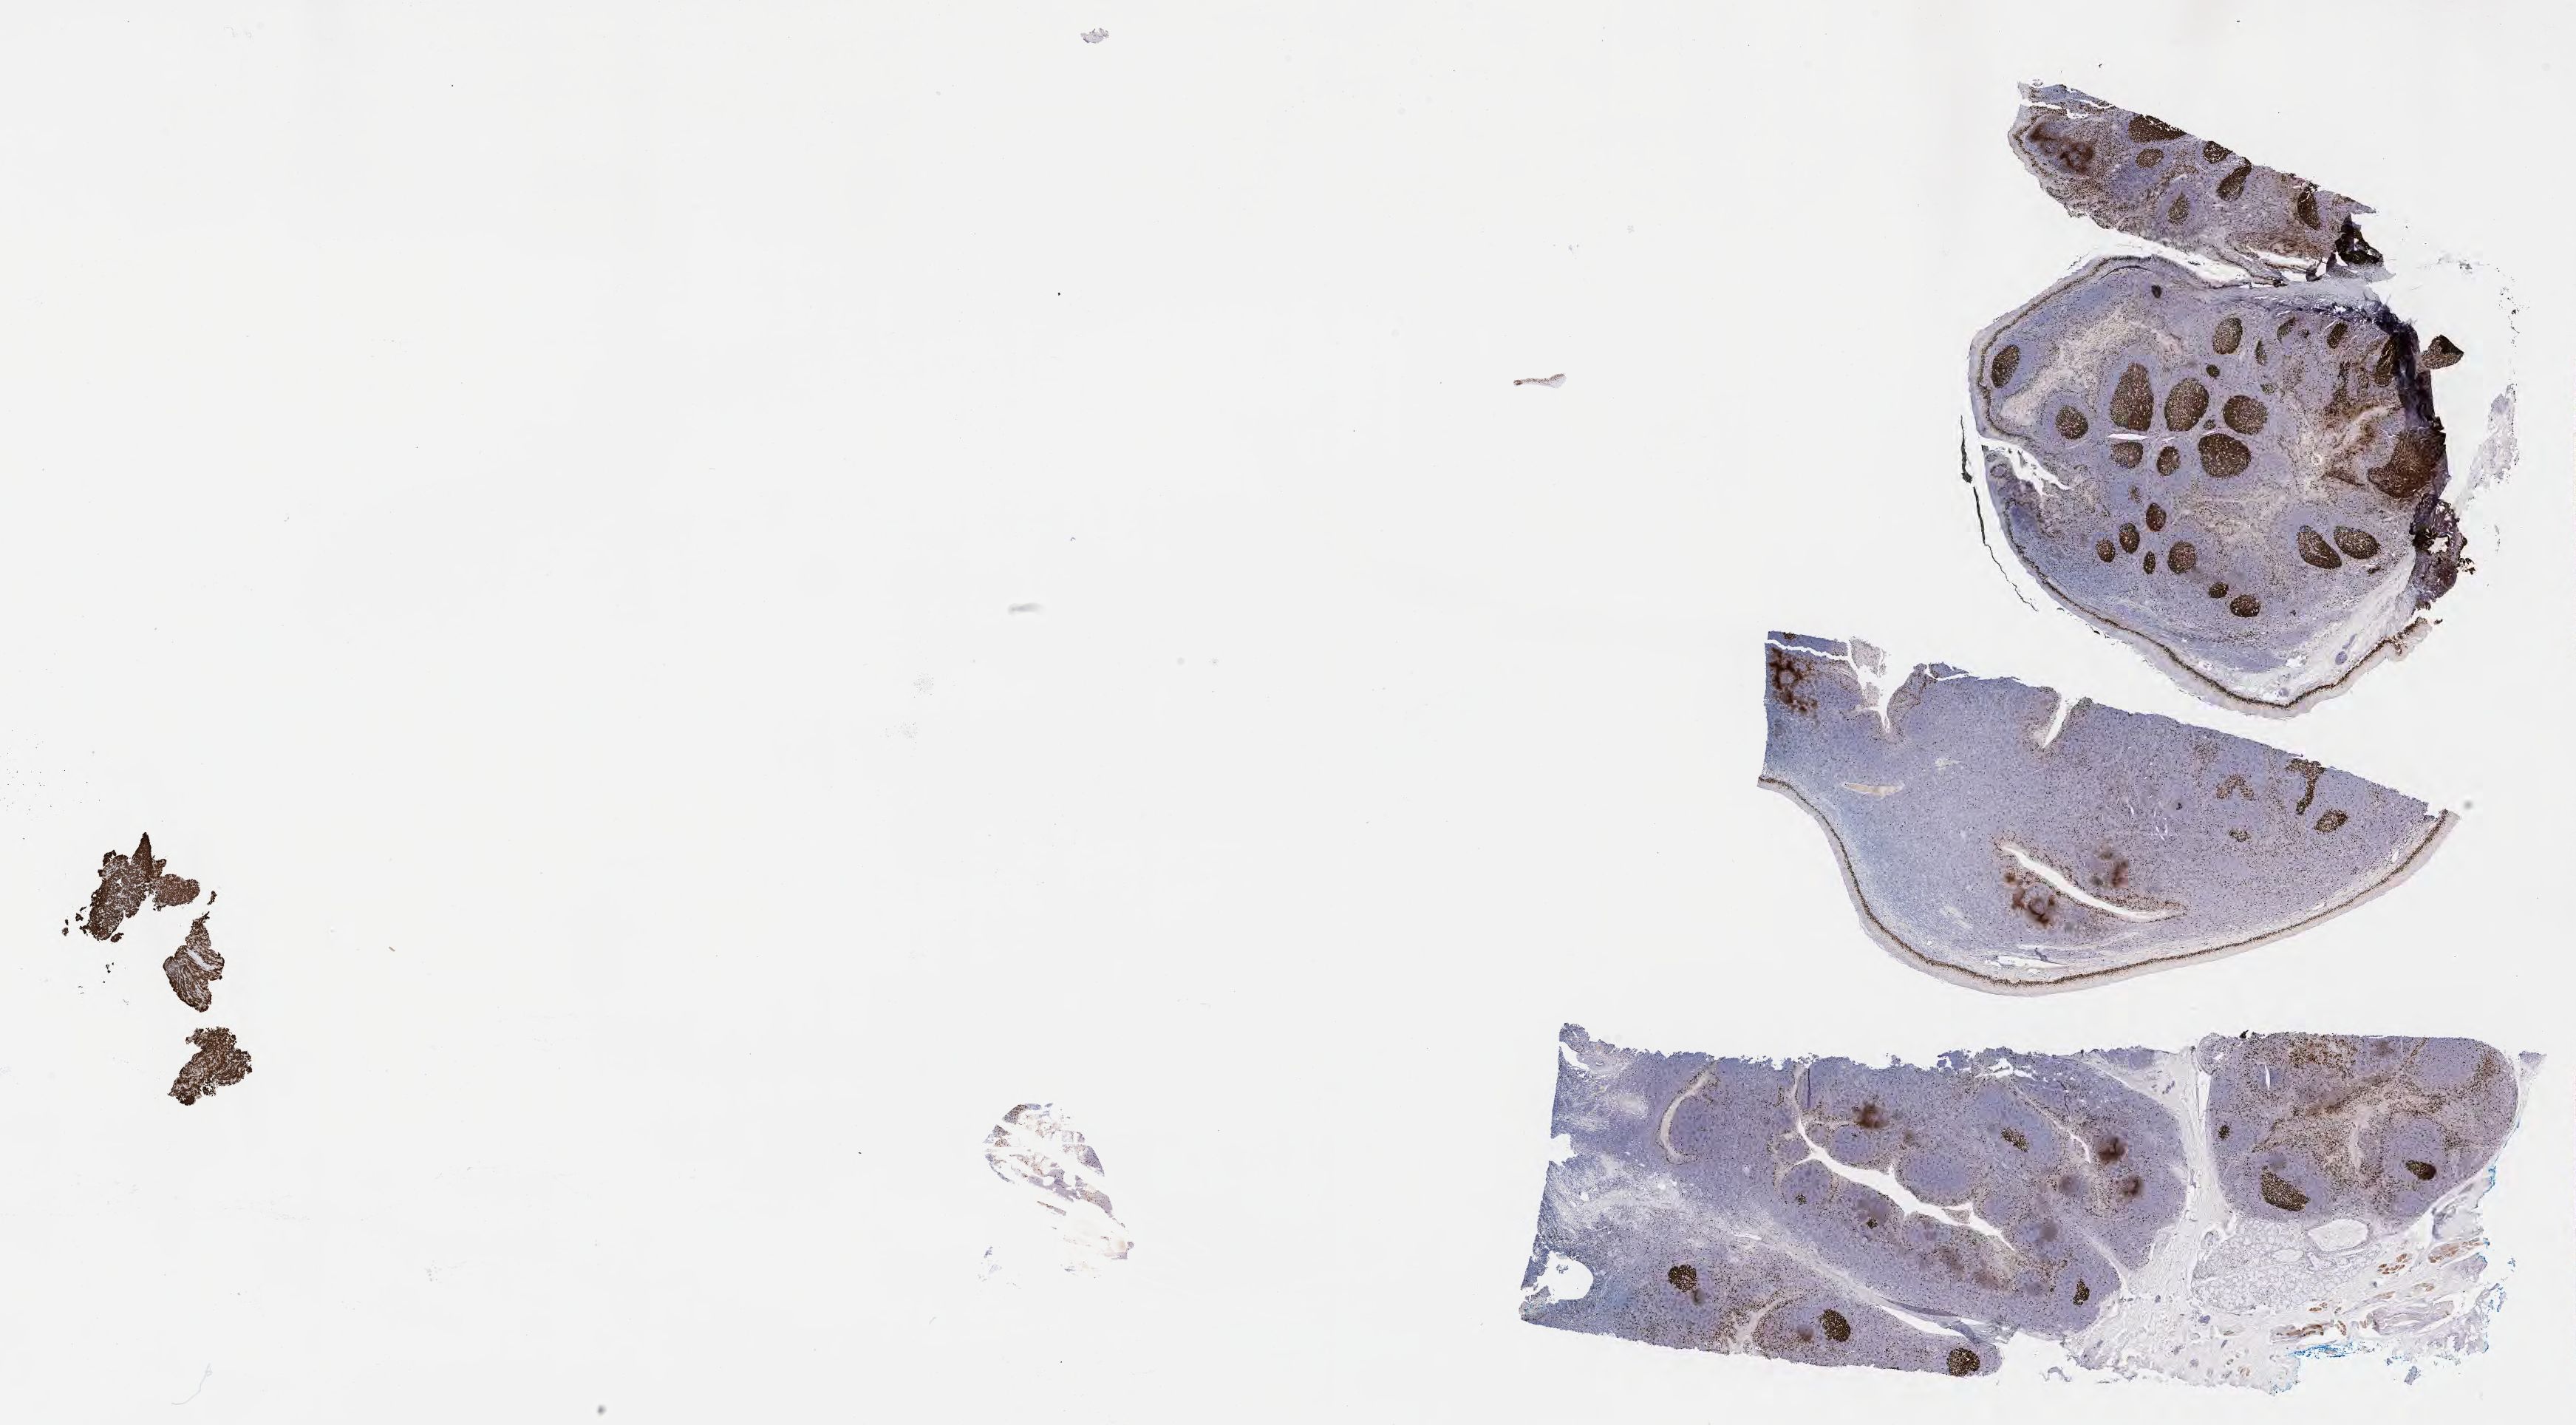
Whole-slide image, immunohistochemical stain for Ki-67 — whole scanned area (about 28.2 x 15.6 mm) shown as a low-resolution overview, tumor tissue, anatomic site: abdomen proper. Male, age 6 years at initial diagnosis.
- diagnosis: Burkitt lymphoma, NOS